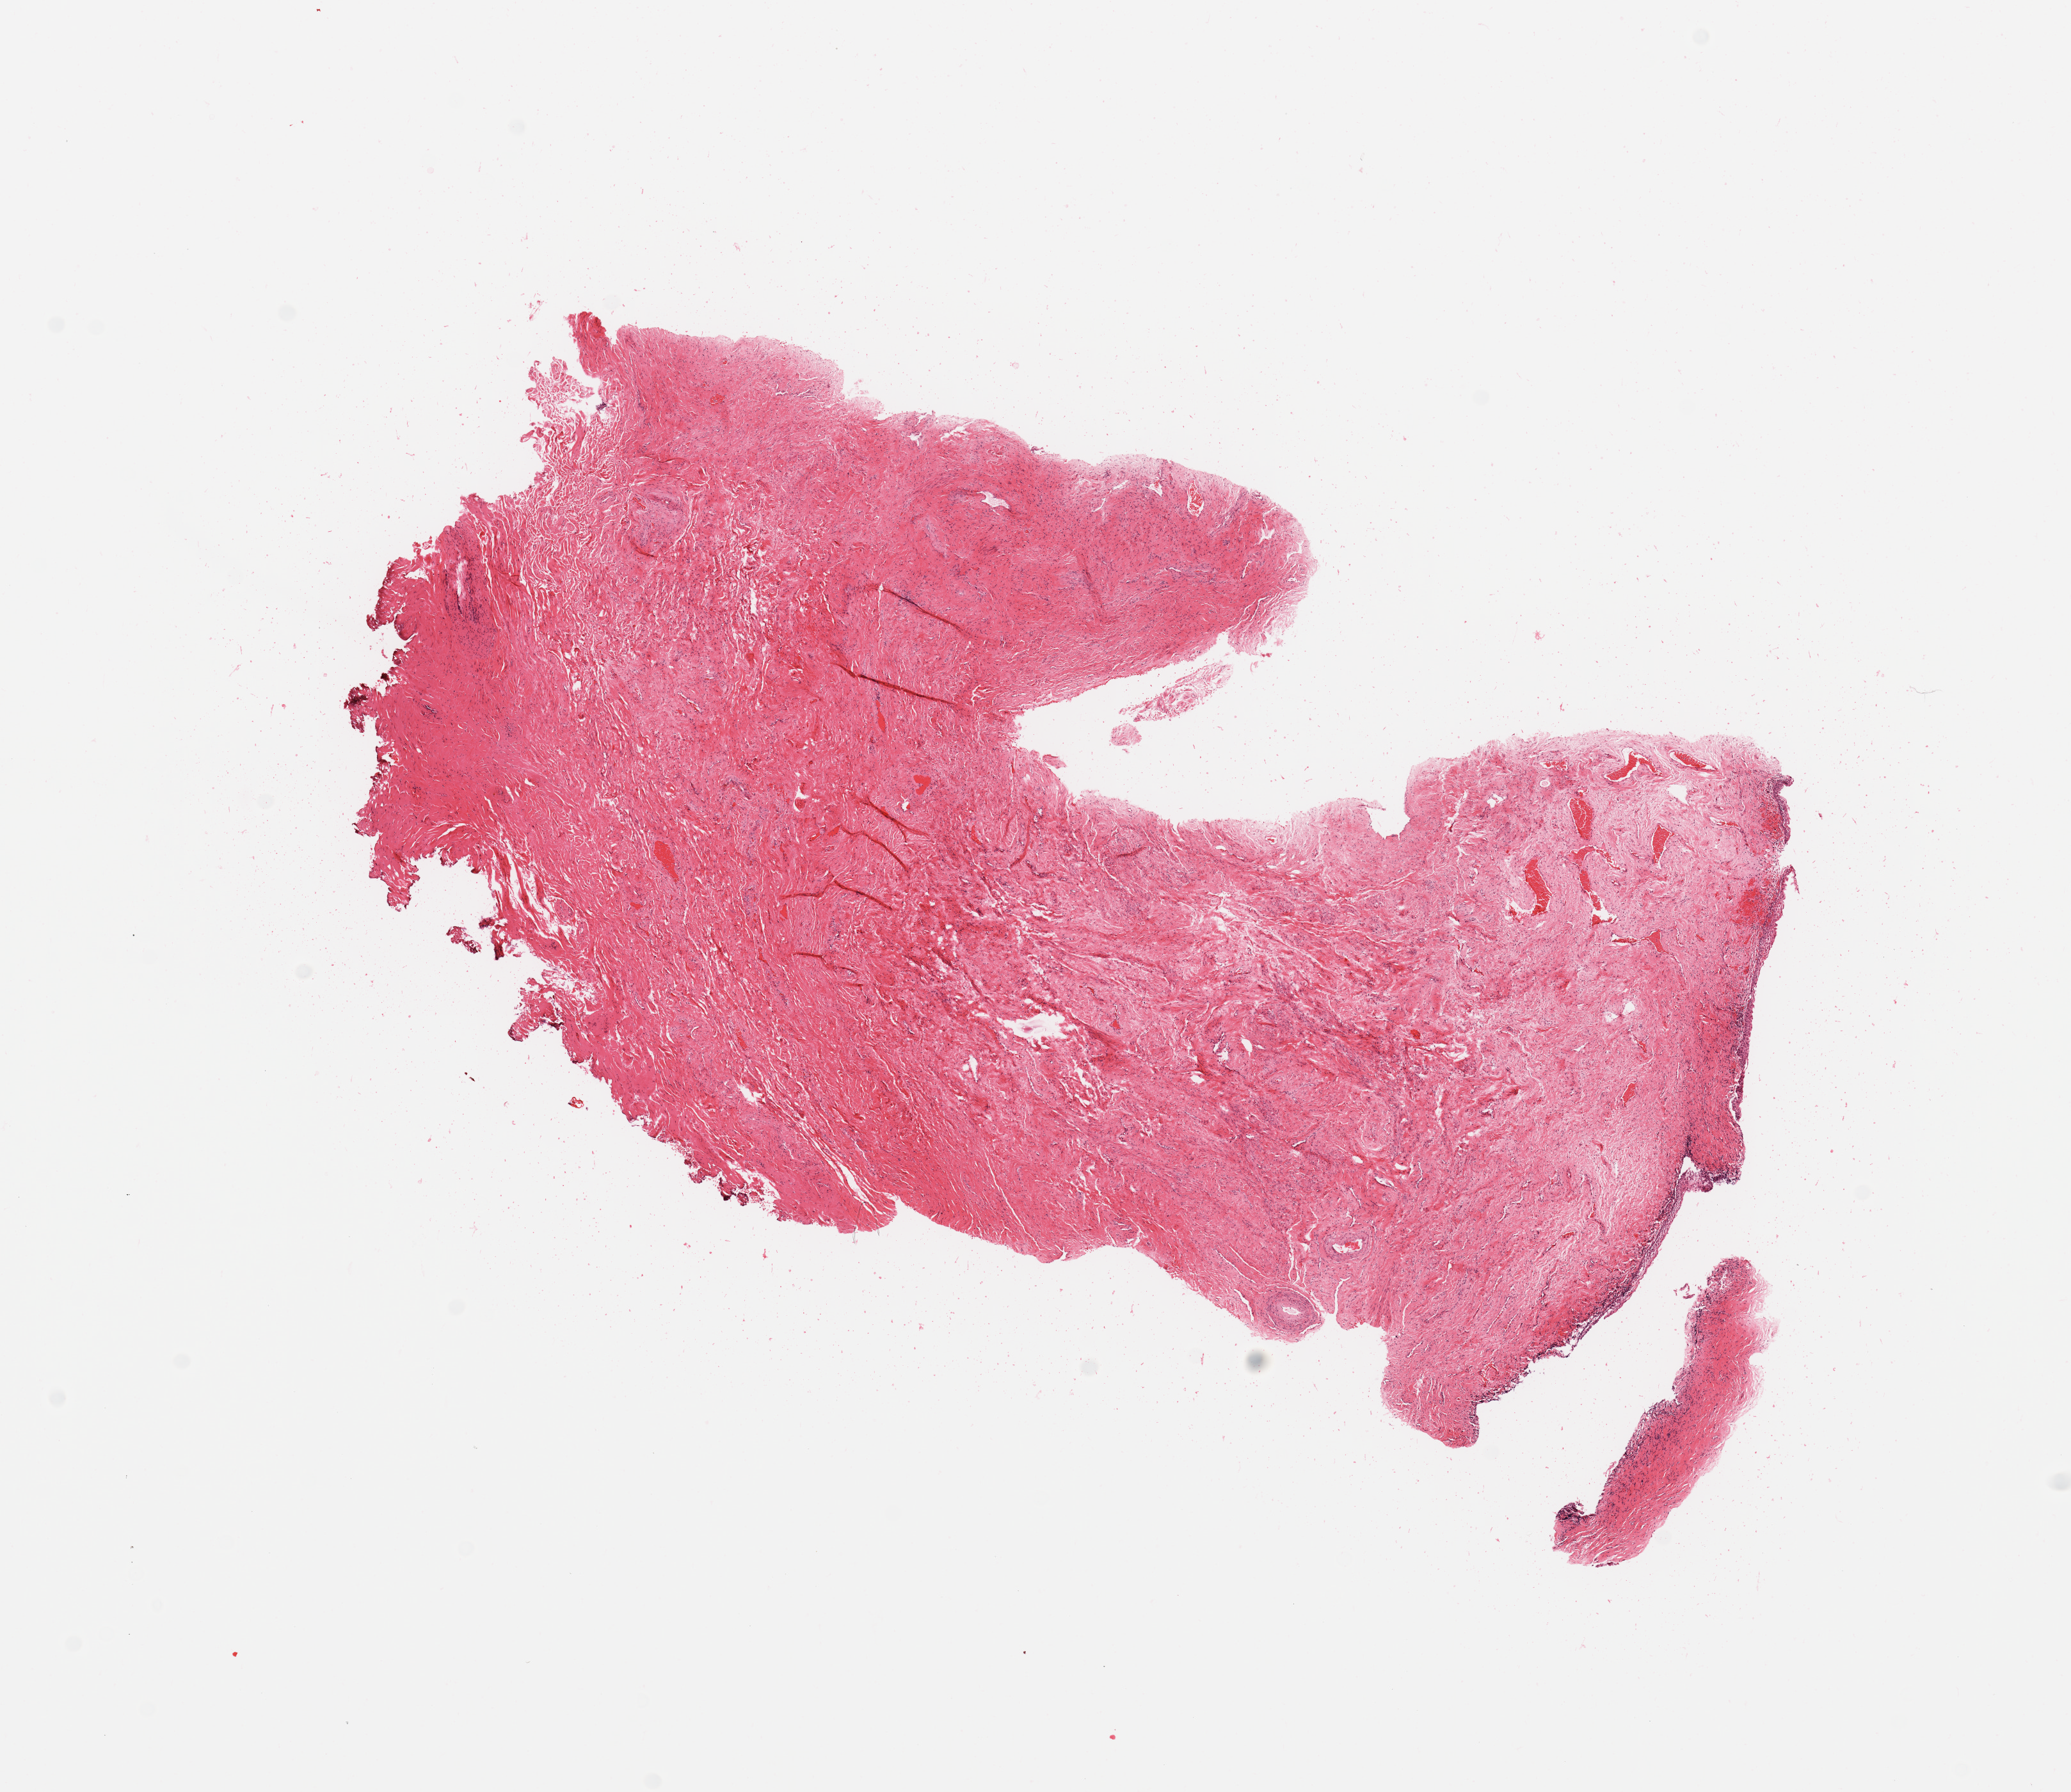
Whole-slide histology image, H&E, shown as a low-resolution overview of the whole scanned area (about 12.8 x 11.1 mm, acquisition: 20x scan); tumour tissue sample, uterus. Patient: female, age 74 years. Histologic grade: G1 (well differentiated).
Diagnosis: Endometrioid adenocarcinoma, NOS. AJCC pathologic stage: I.